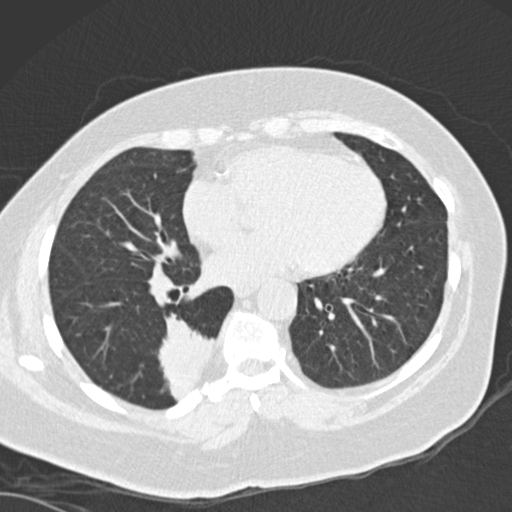
Chest CT (low-dose screening protocol), one axial image, baseline annual screen, lung window (W 1500 / L -600 HU), 512 × 512 image matrix, field of view 328 × 328 mm. Female, age 66 years at enrolment.
Lesion marked by an expert reader, box from (x=149, y=320) to (x=227, y=401) px. The screening reader recorded 3 non-calcified nodules or masses ≥4 mm on this exam (left lower lobe, left lower lobe, right lower lobe); which of them this box marks is not recorded. Participant outcome: lung cancer diagnosed 67 days after this screen — adenocarcinoma, NOS, right lower lobe, well differentiated (G1), stage IB (AJCC 6th edition), 55 mm at pathology.